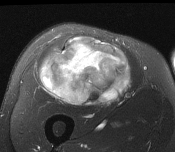
MRI of an extremity soft-tissue mass, one axial slice; slice 89 of 116 in the series (ordered by position); T2-weighted fat-saturated; MR volume resampled by the dataset authors to the PET/CT grid (not the native acquisition matrix); 3.27 mm slice thickness; 175 × 152 image matrix. Male patient. Case-level facts recorded for this patient, not image findings: histological type: pleiomorphic leiomyosarcoma; grade: intermediate; site of the primary tumour: right thigh.
Annotated regions visible in this slice (expert contour drawn on MRI and transferred to this co-registered scan by the dataset authors):
- gross tumour volume including surrounding oedema: box from (x=40, y=38) to (x=130, y=107) px
- gross tumour volume (mass): (x=40, y=38)–(x=130, y=107)